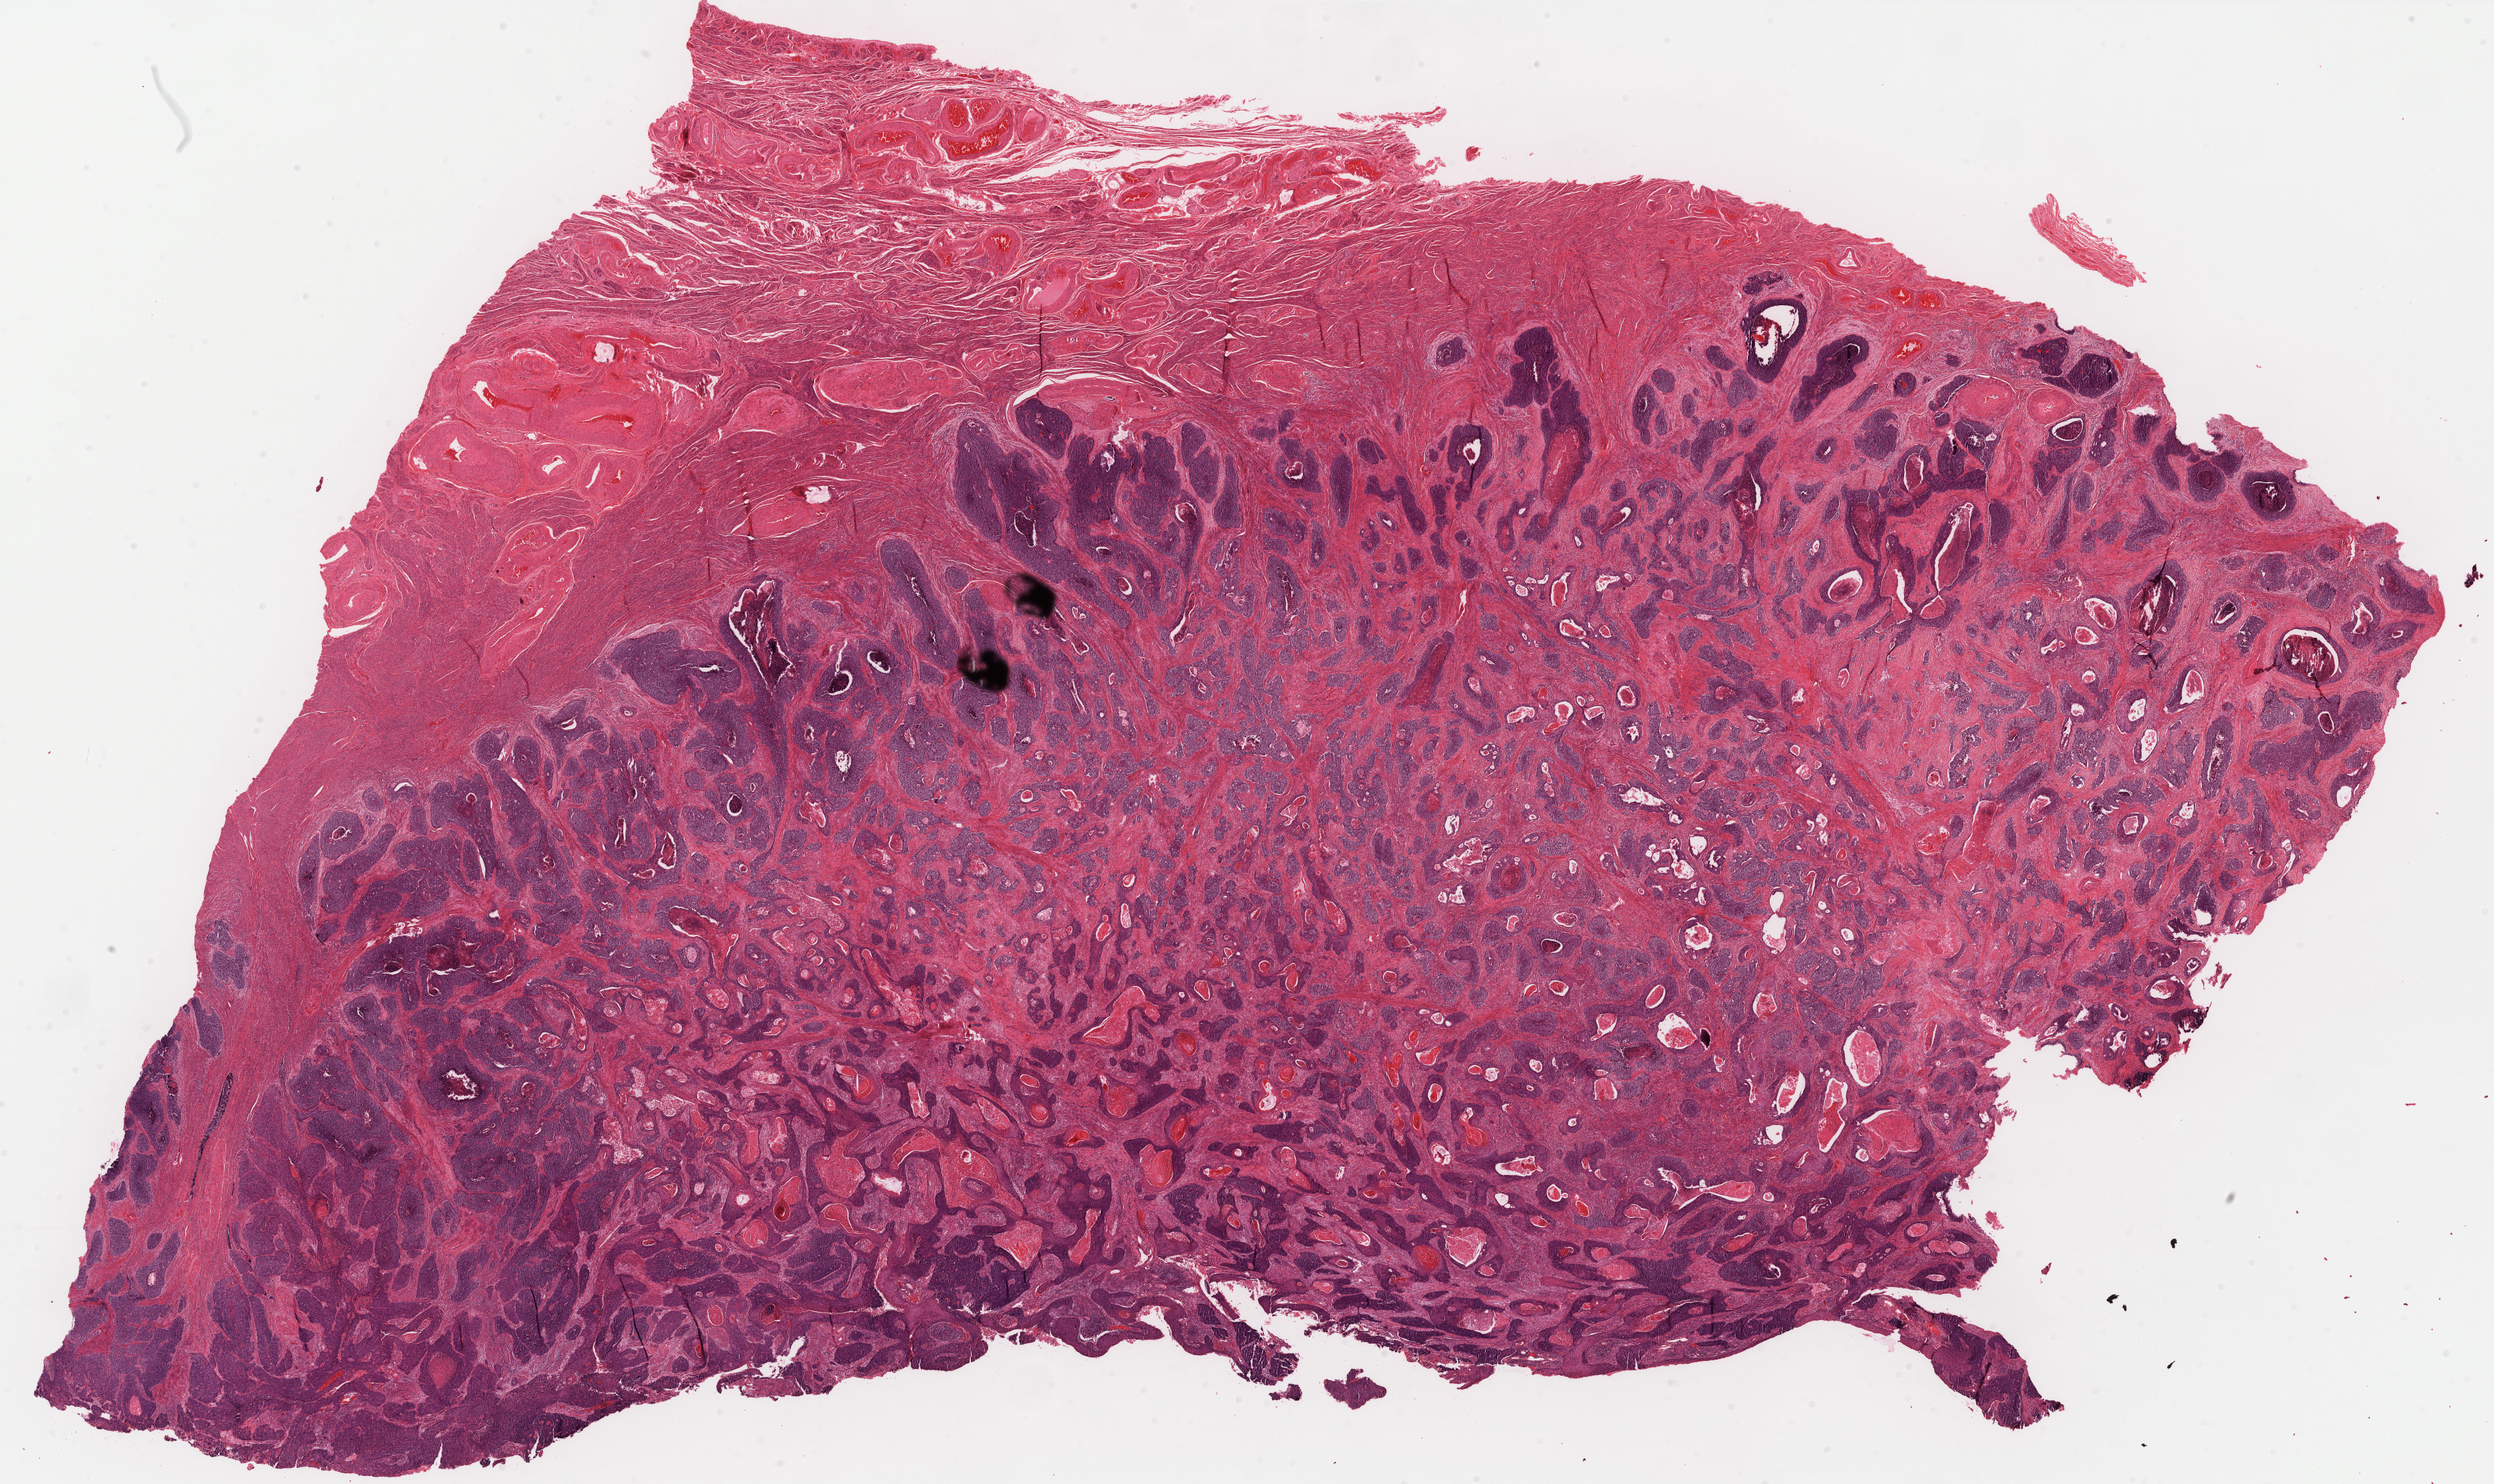
Digitized H&E tissue section (whole slide), low-resolution overview of the scanned area, about 30.0 x 17.9 mm; formalin-fixed paraffin-embedded (FFPE) diagnostic section; sample: primary tumour, cervix. Patient: female, age at initial diagnosis 64 years. Histologic grade: G2 (moderately differentiated).
Pathologic diagnosis: Squamous cell carcinoma, large cell, nonkeratinizing, NOS (cervix uteri). Lymph nodes positive (case pathology): 2 of 38 examined. FIGO stage: IB2.